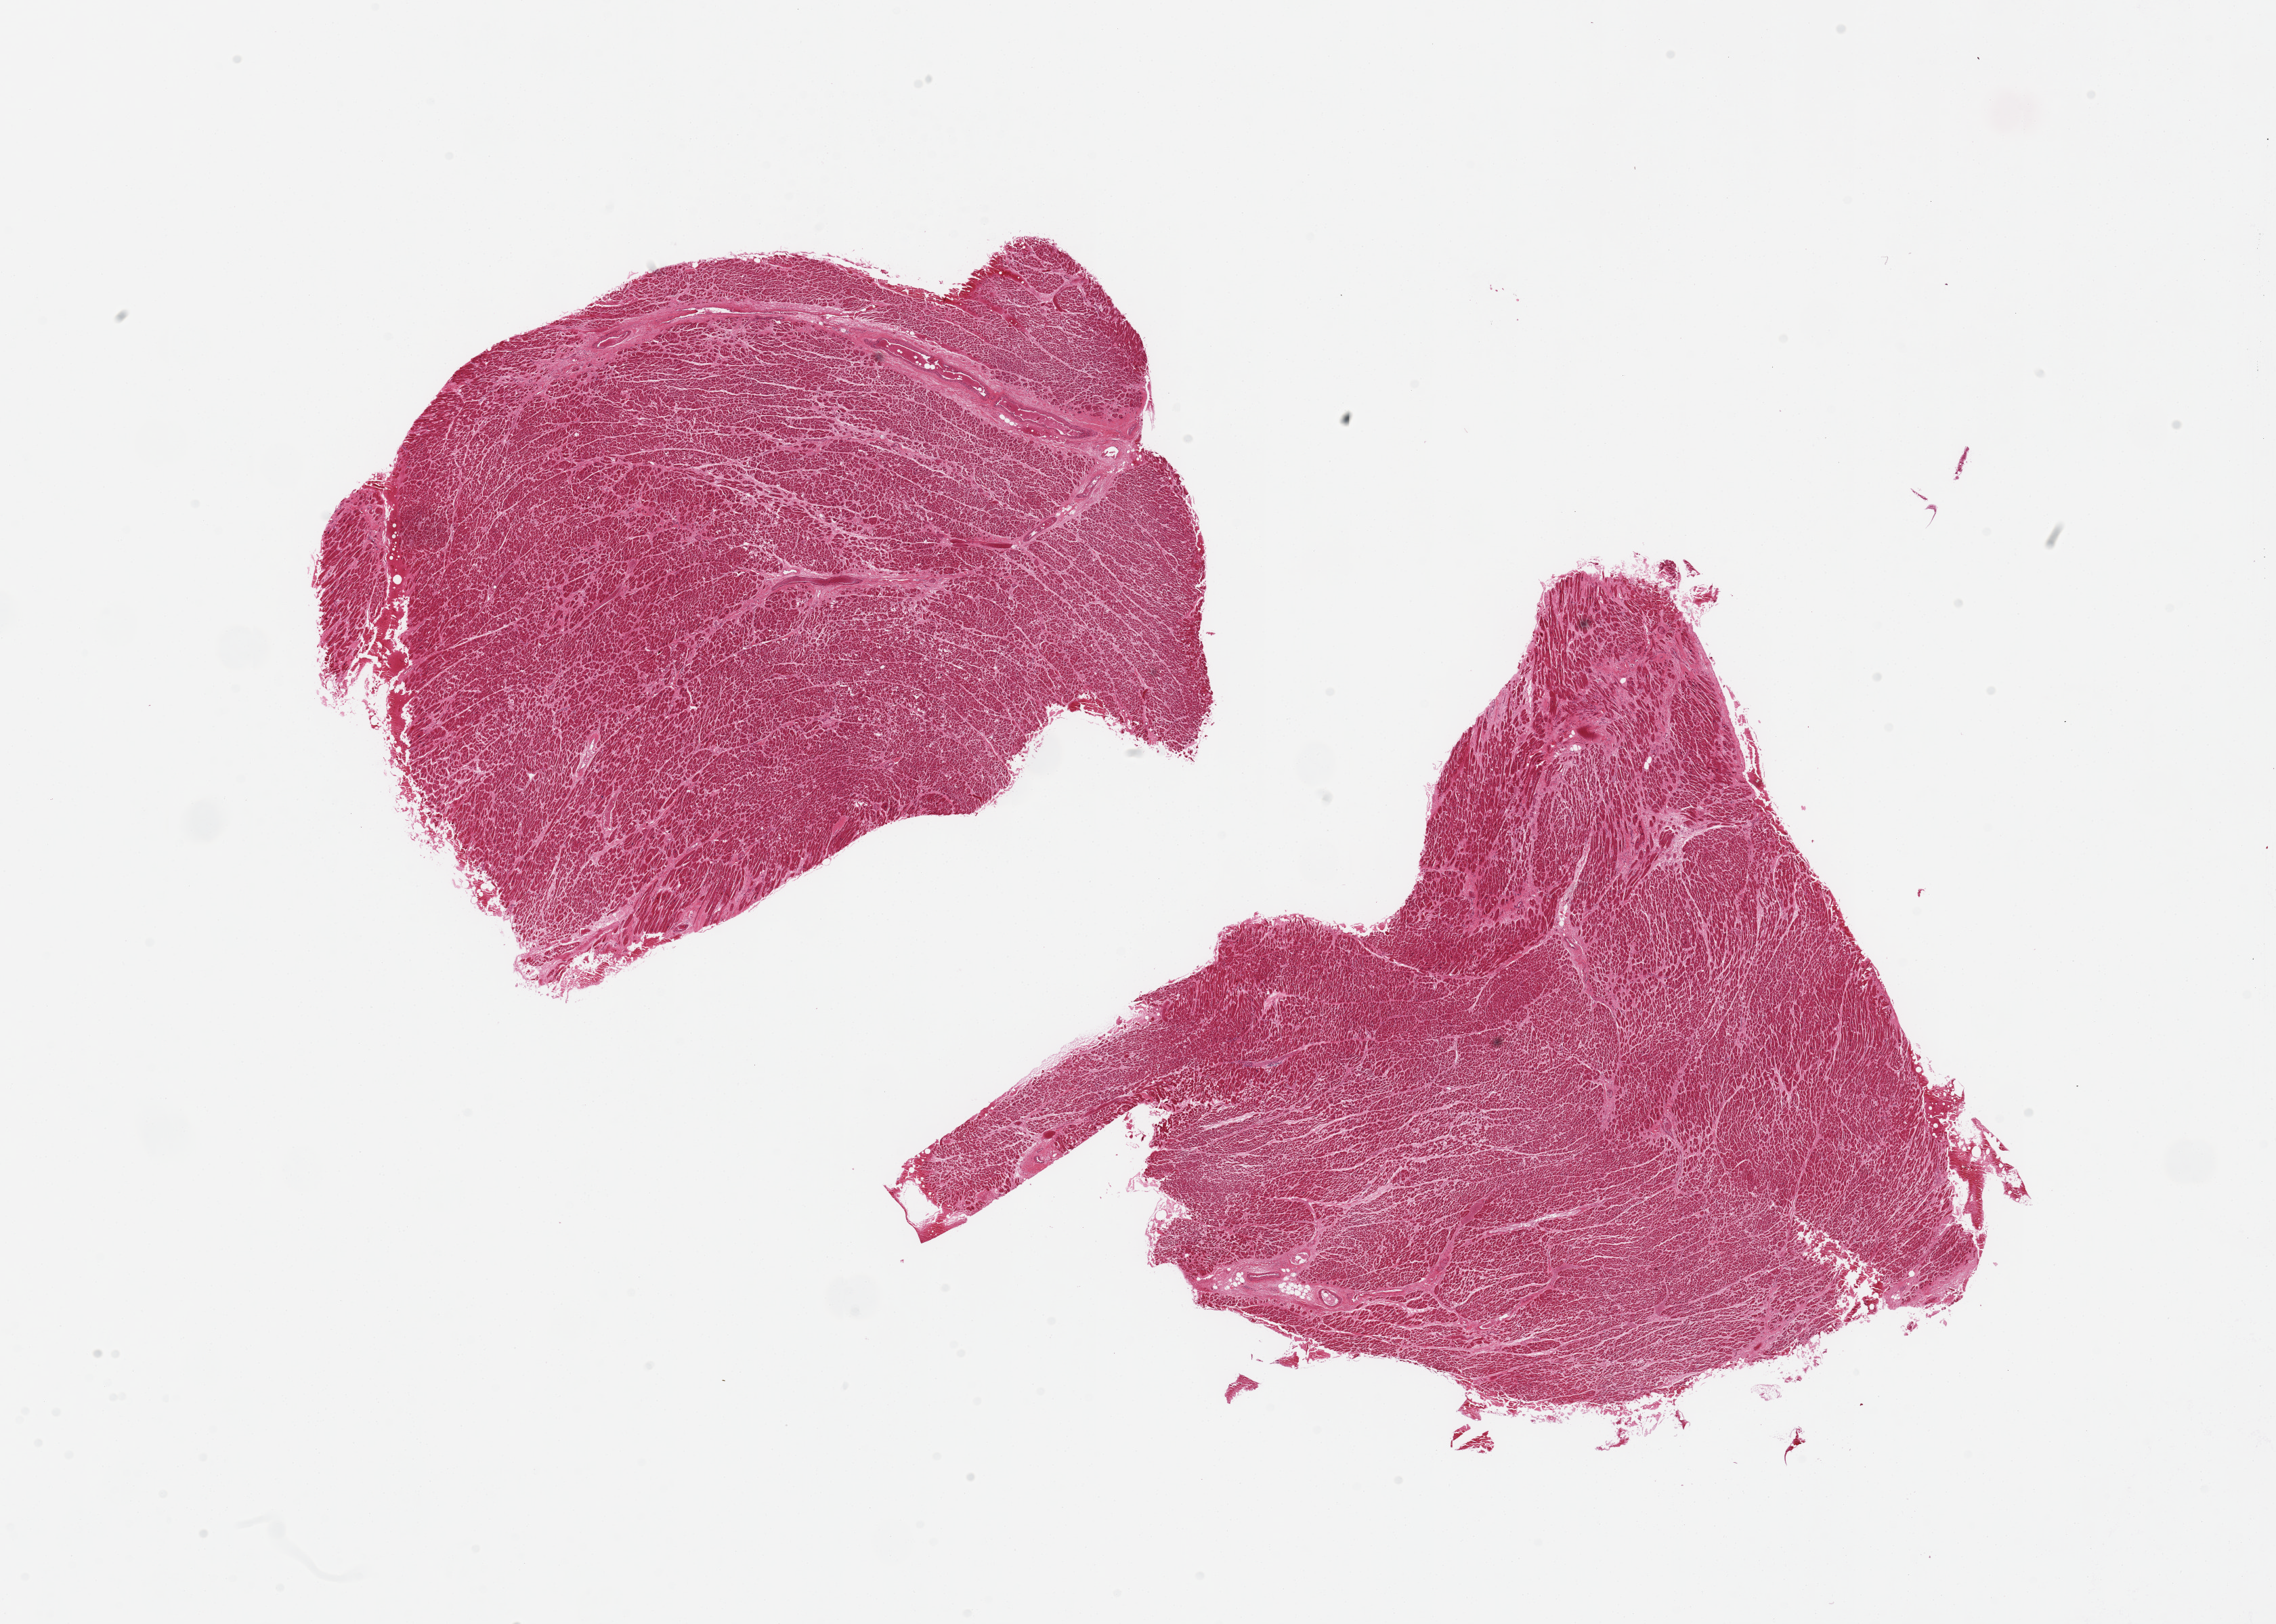
Digitized haematoxylin and eosin-stained section, brightfield, shown as a low-resolution overview of the whole scanned area (about 26.6 x 19.0 mm, slide scanned at 20x), PAXgene-fixed, paraffin-embedded tissue, target tissue: heart, tissue donor sample. Male donor.
Pathologist's review note for this sample: 2 pieces, patchy in terstitial fibrosis, focal remote microinfarct.